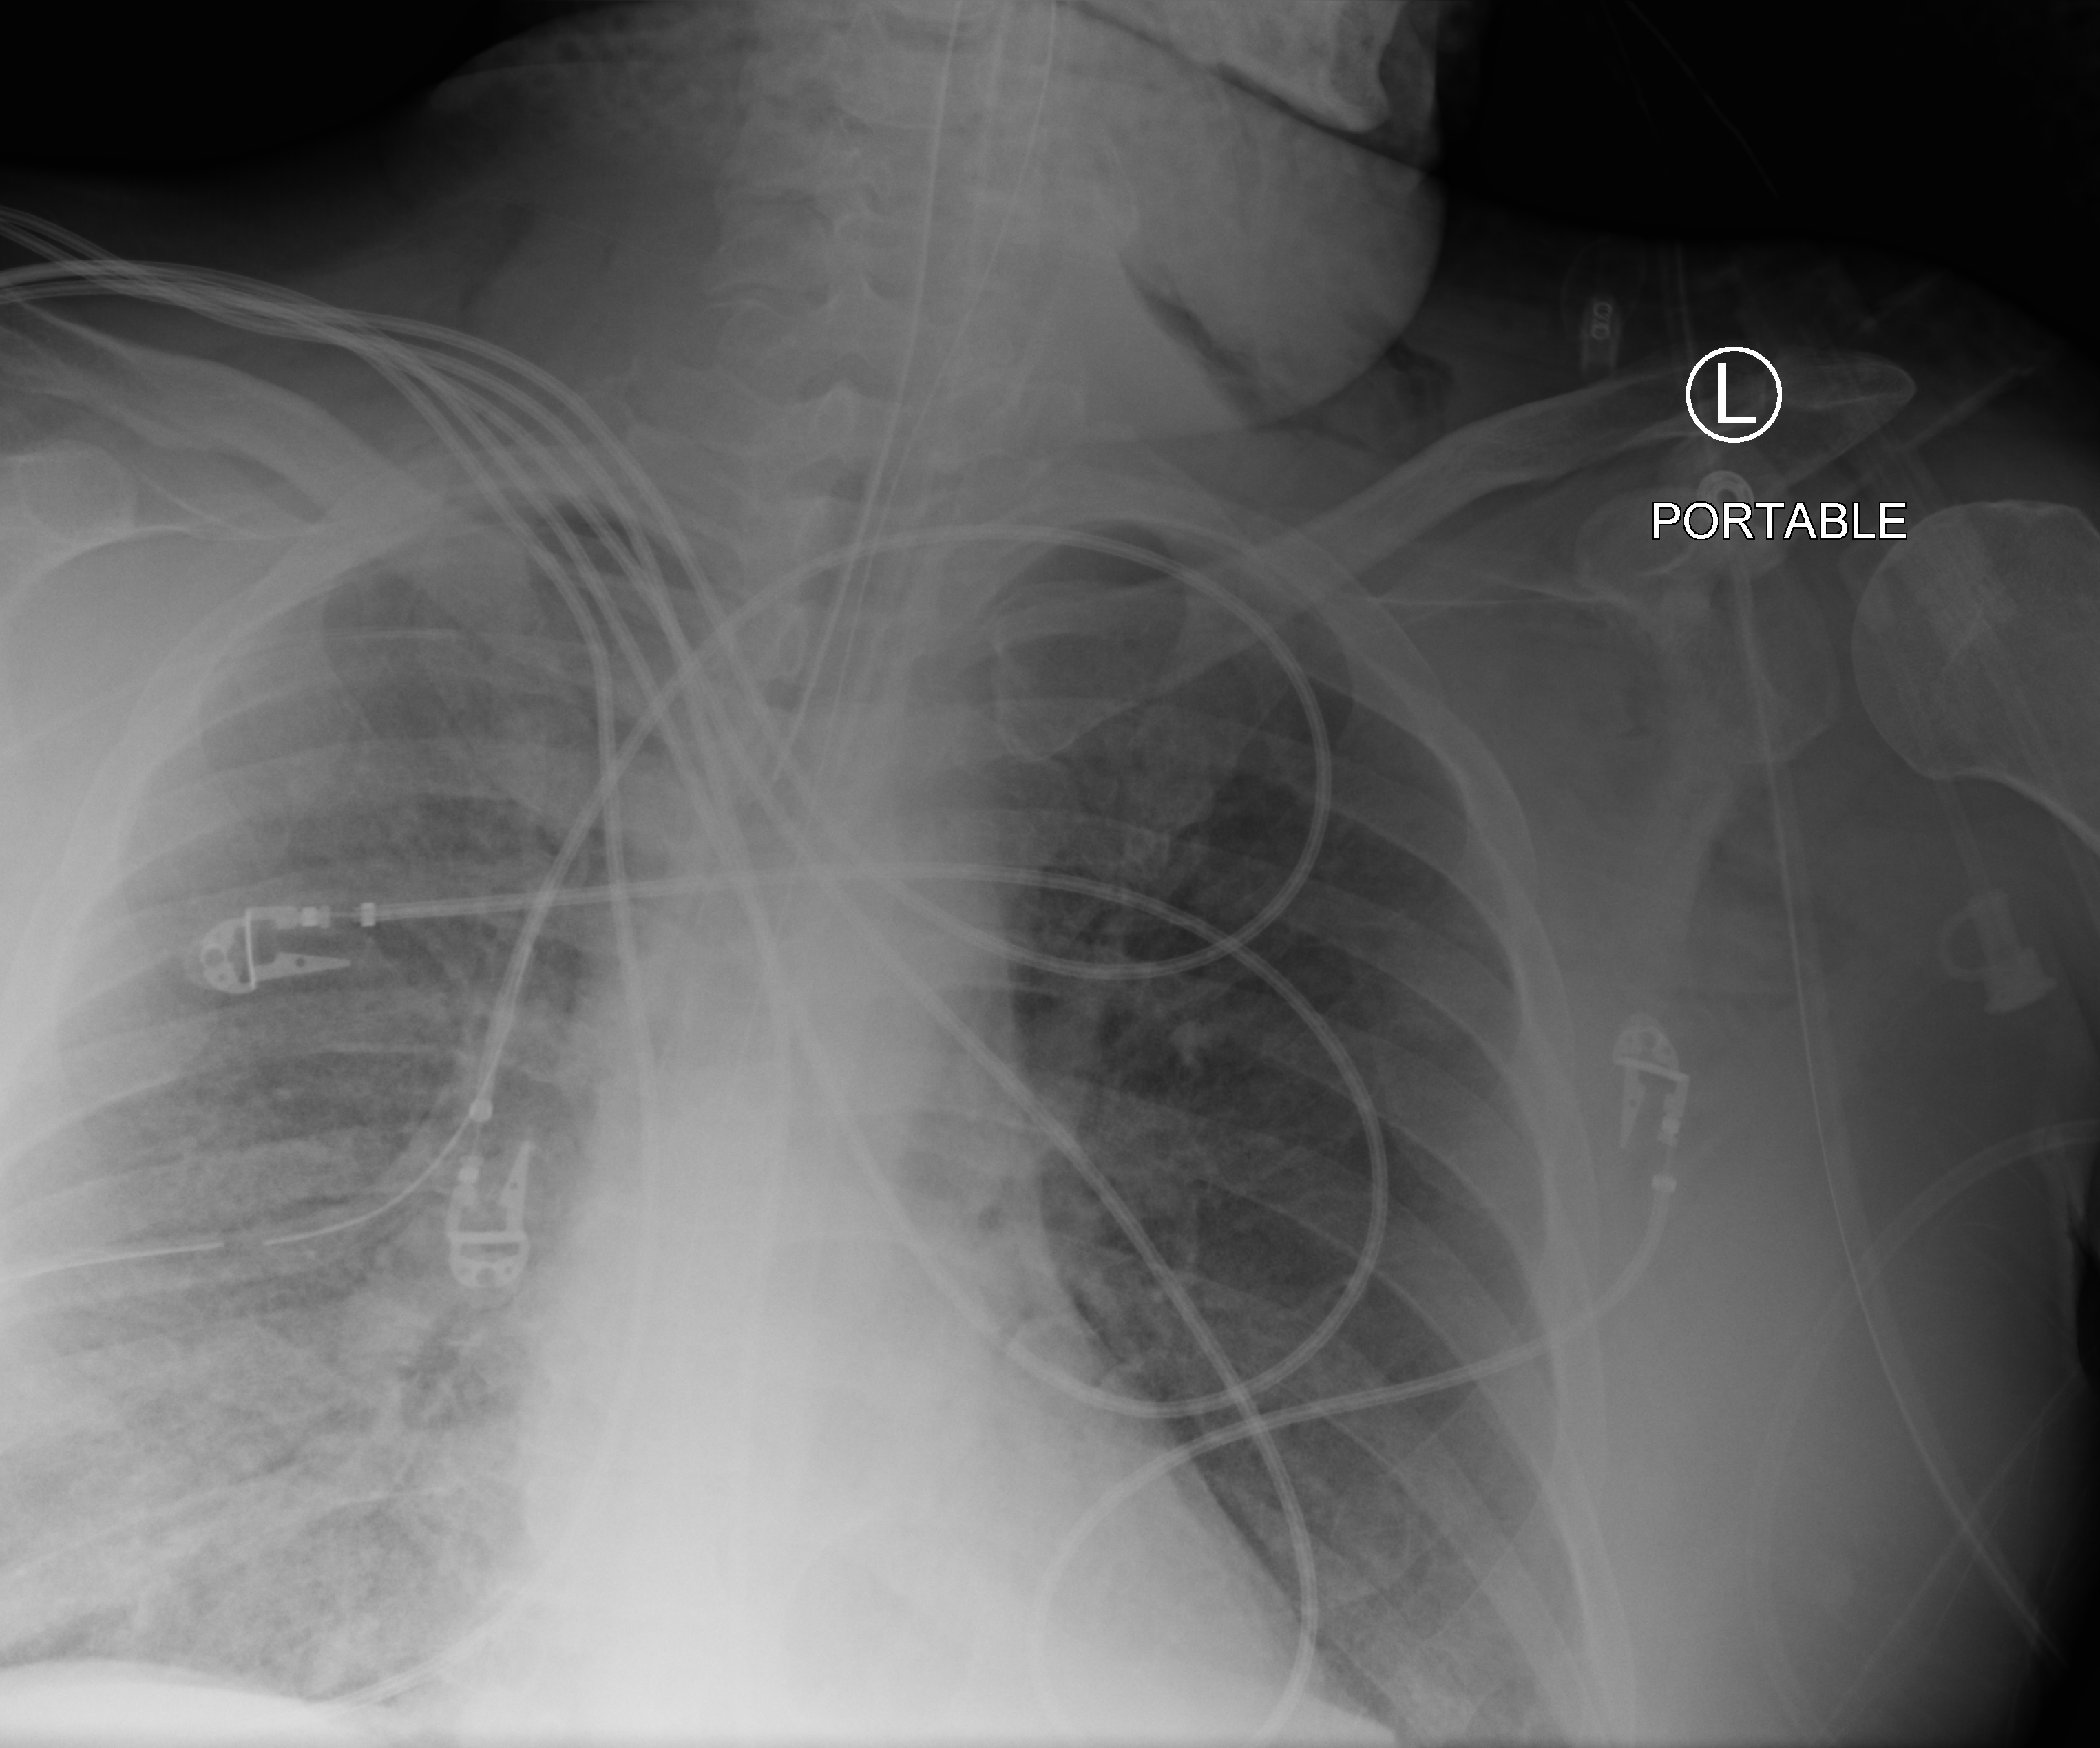
Chest X-ray (portable), anteroposterior (AP) projection. Adult patient hospitalised with COVID-19, age 18–59 years.
Admission-level facts for this patient (not findings on this image; timing relative to this image not recorded): mechanically ventilated during this hospital stay: yes; admitted to intensive care during this hospital stay: yes; COPD (admission record): no.